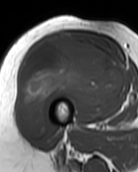
MRI of an extremity soft-tissue mass, one axial slice. Slice 50 of 99 in the series (ordered by position). MR volume resampled by the dataset authors to the PET/CT grid (not the native acquisition matrix). 138 × 172 image matrix, field of view 135 × 168 mm. Female patient. Case-level facts recorded for this patient, not image findings: histological type: pleiomorphic undifferentiated sarcoma; grade: high; site of the primary tumour: right quadricep.
Annotated regions visible in this slice (expert contour drawn on MRI and transferred to this co-registered scan by the dataset authors):
- gross tumour volume including surrounding oedema: box from (x=18, y=32) to (x=125, y=136) px
- gross tumour volume (mass): (x=18, y=32)–(x=125, y=136)